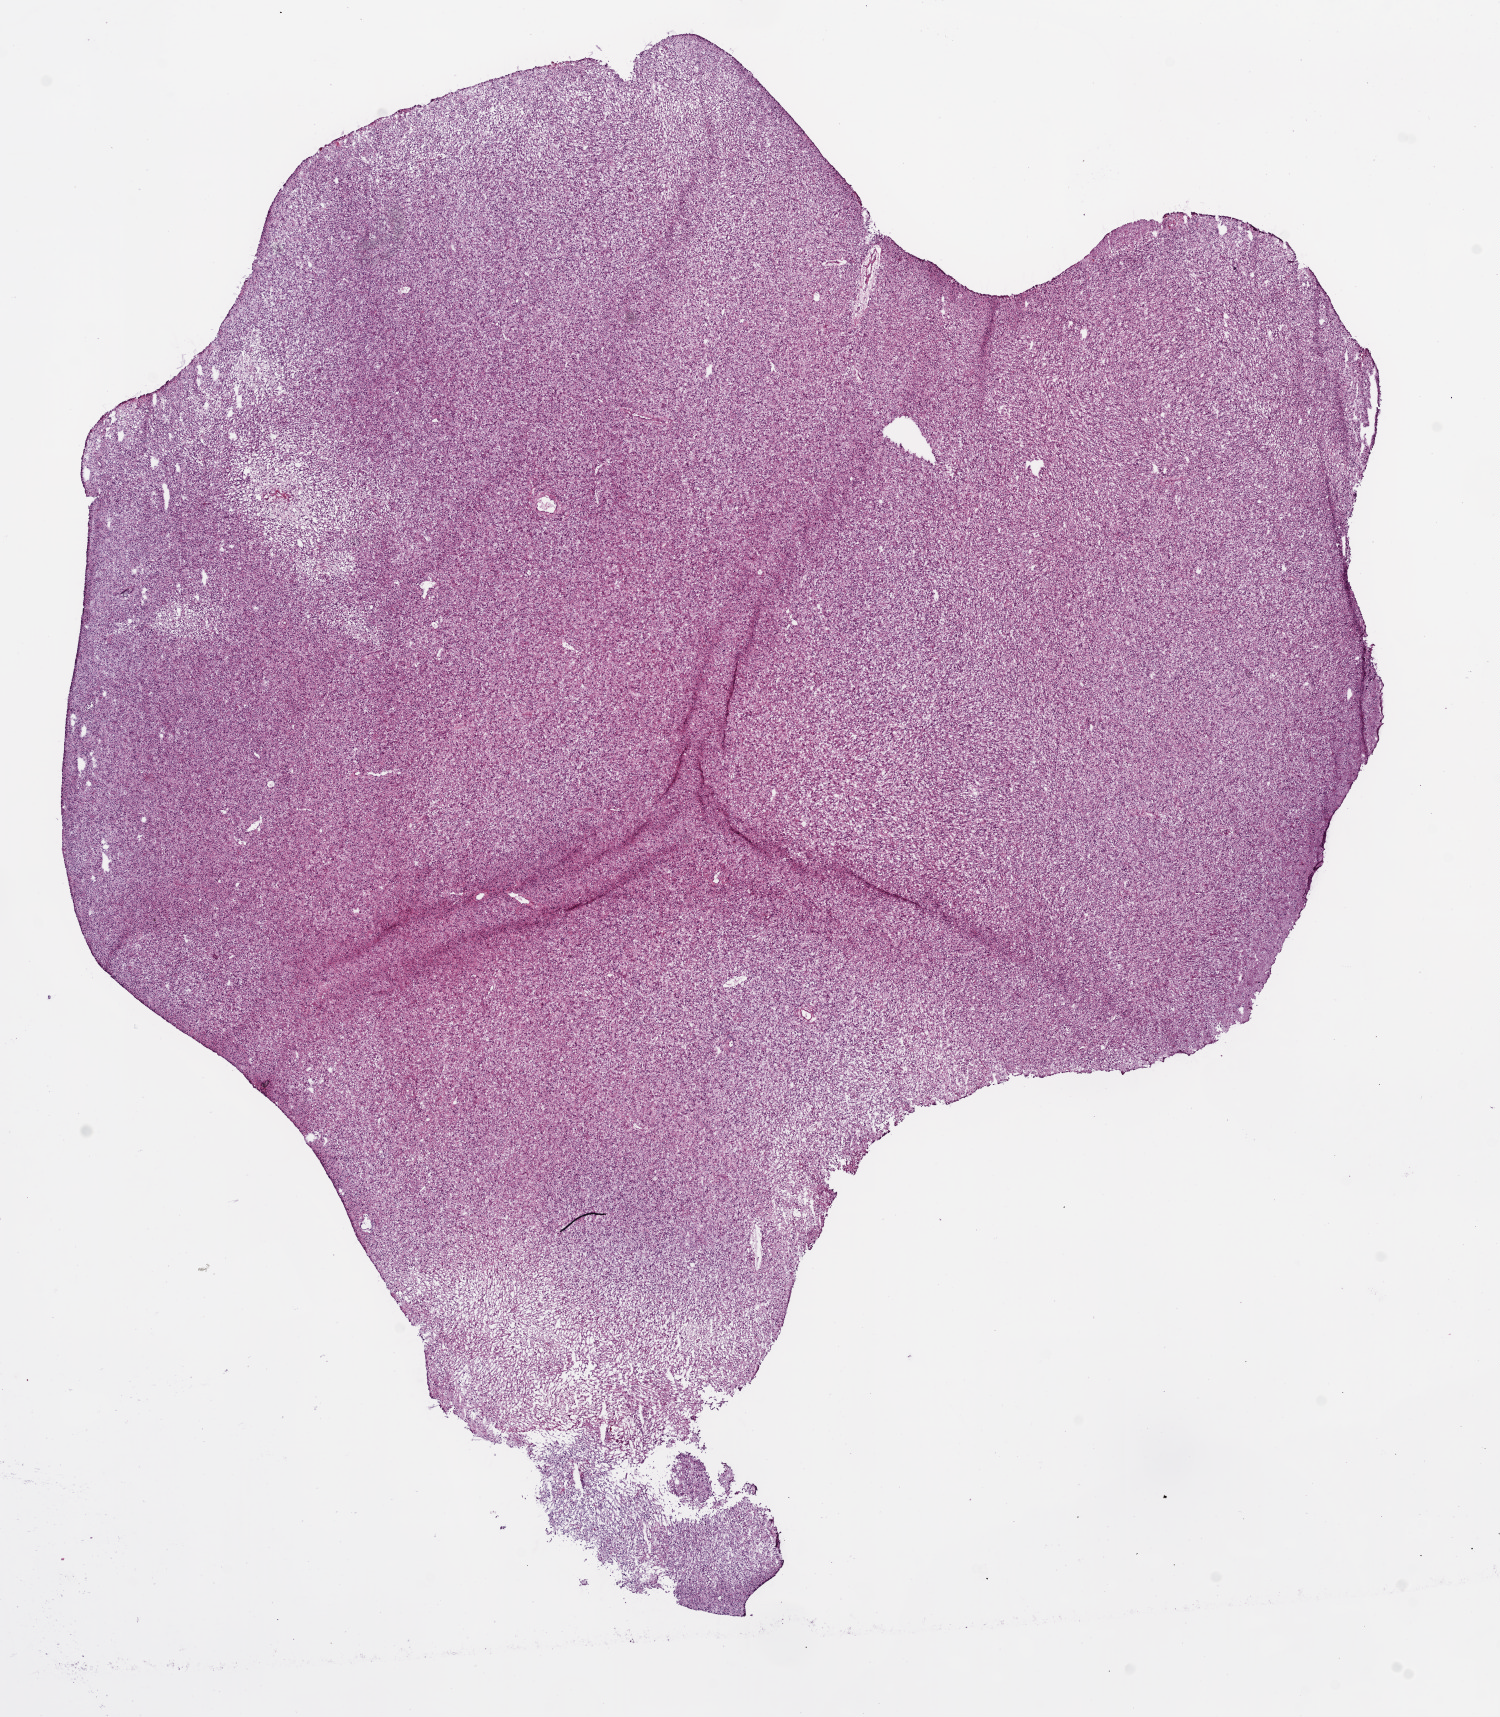
Digitized H&E-stained tissue section (whole slide), shown as a low-resolution overview of the whole scanned area (about 12.0 x 13.8 mm); frozen section from the bottom of the tissue portion; sample: primary tumour, brain. Female patient; age at initial diagnosis 60 years. Pathologist review of this section (percent, as recorded): tumour cells 100%, tumour nuclei 80%, normal cells 0%, stromal cells 0%, necrosis 0%.
Pathologic diagnosis: Glioblastoma.